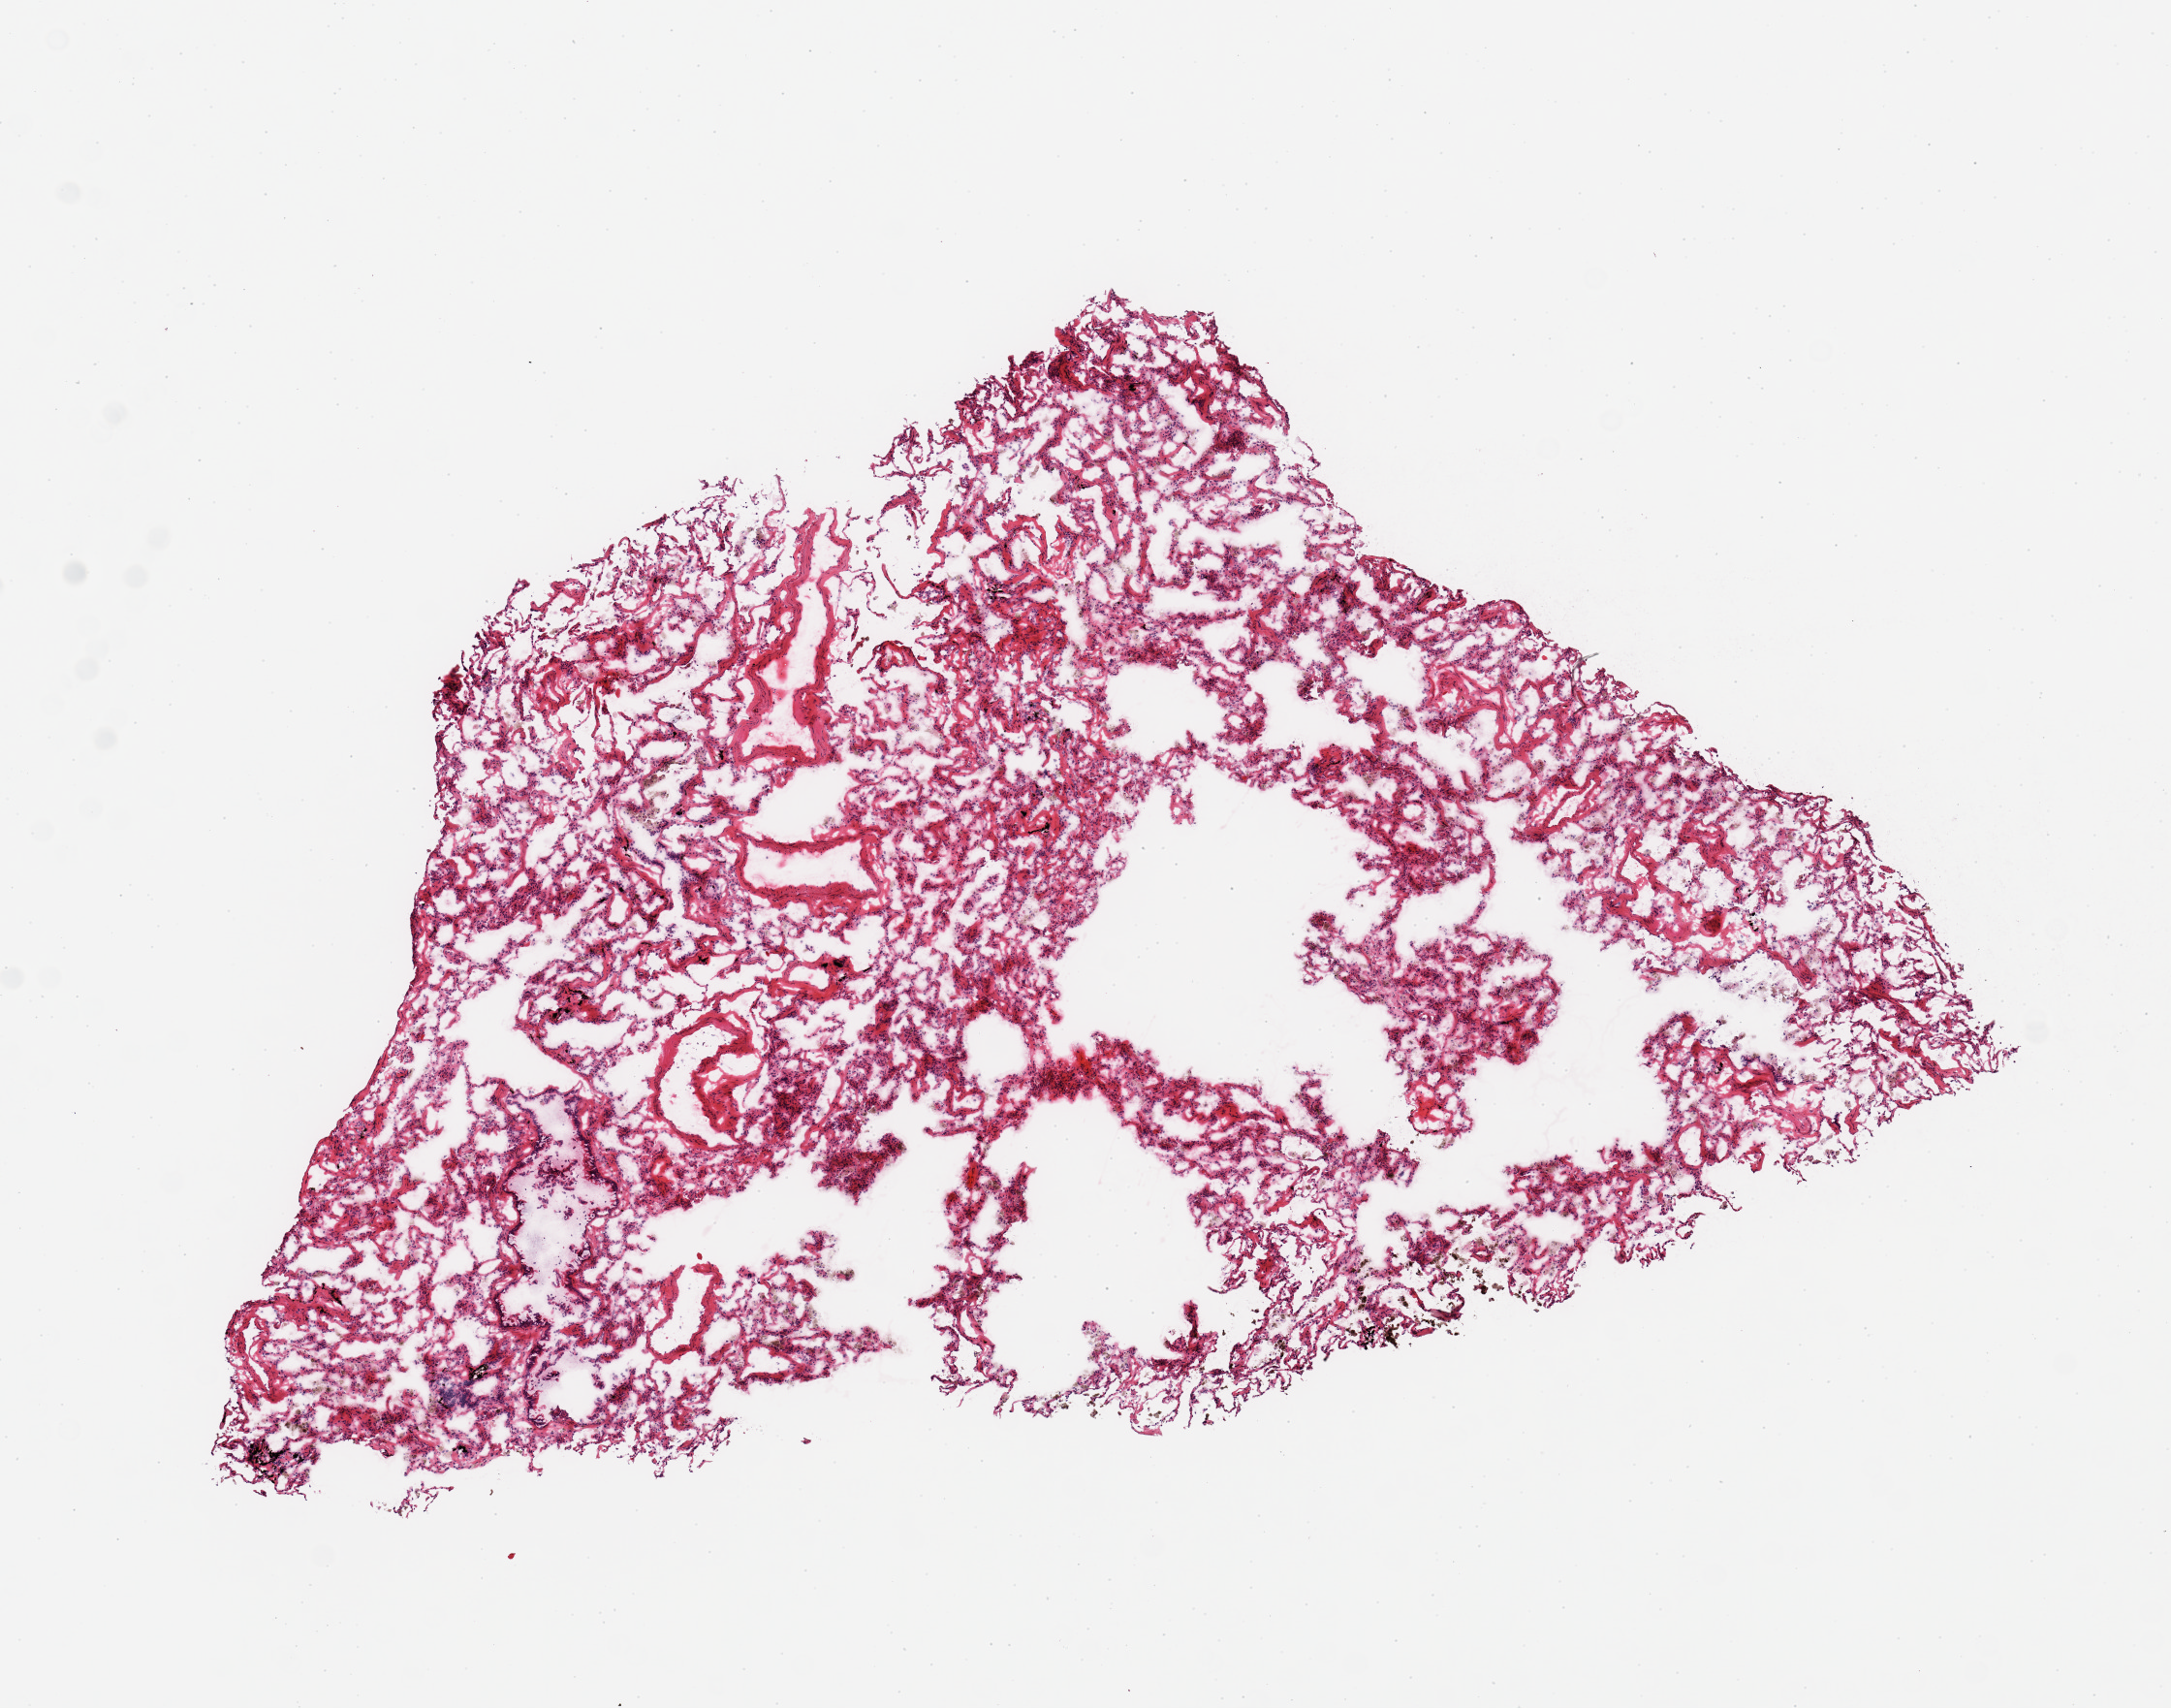
Hematoxylin and eosin (H&E) whole-slide image — whole scanned area (about 8.9 x 7.0 mm, slide scanned at 20x) shown as a low-resolution overview, frozen section, sampled site (target tissue): lung, tissue donor sample.
Pathologist's review note for this sample: 1 piece.